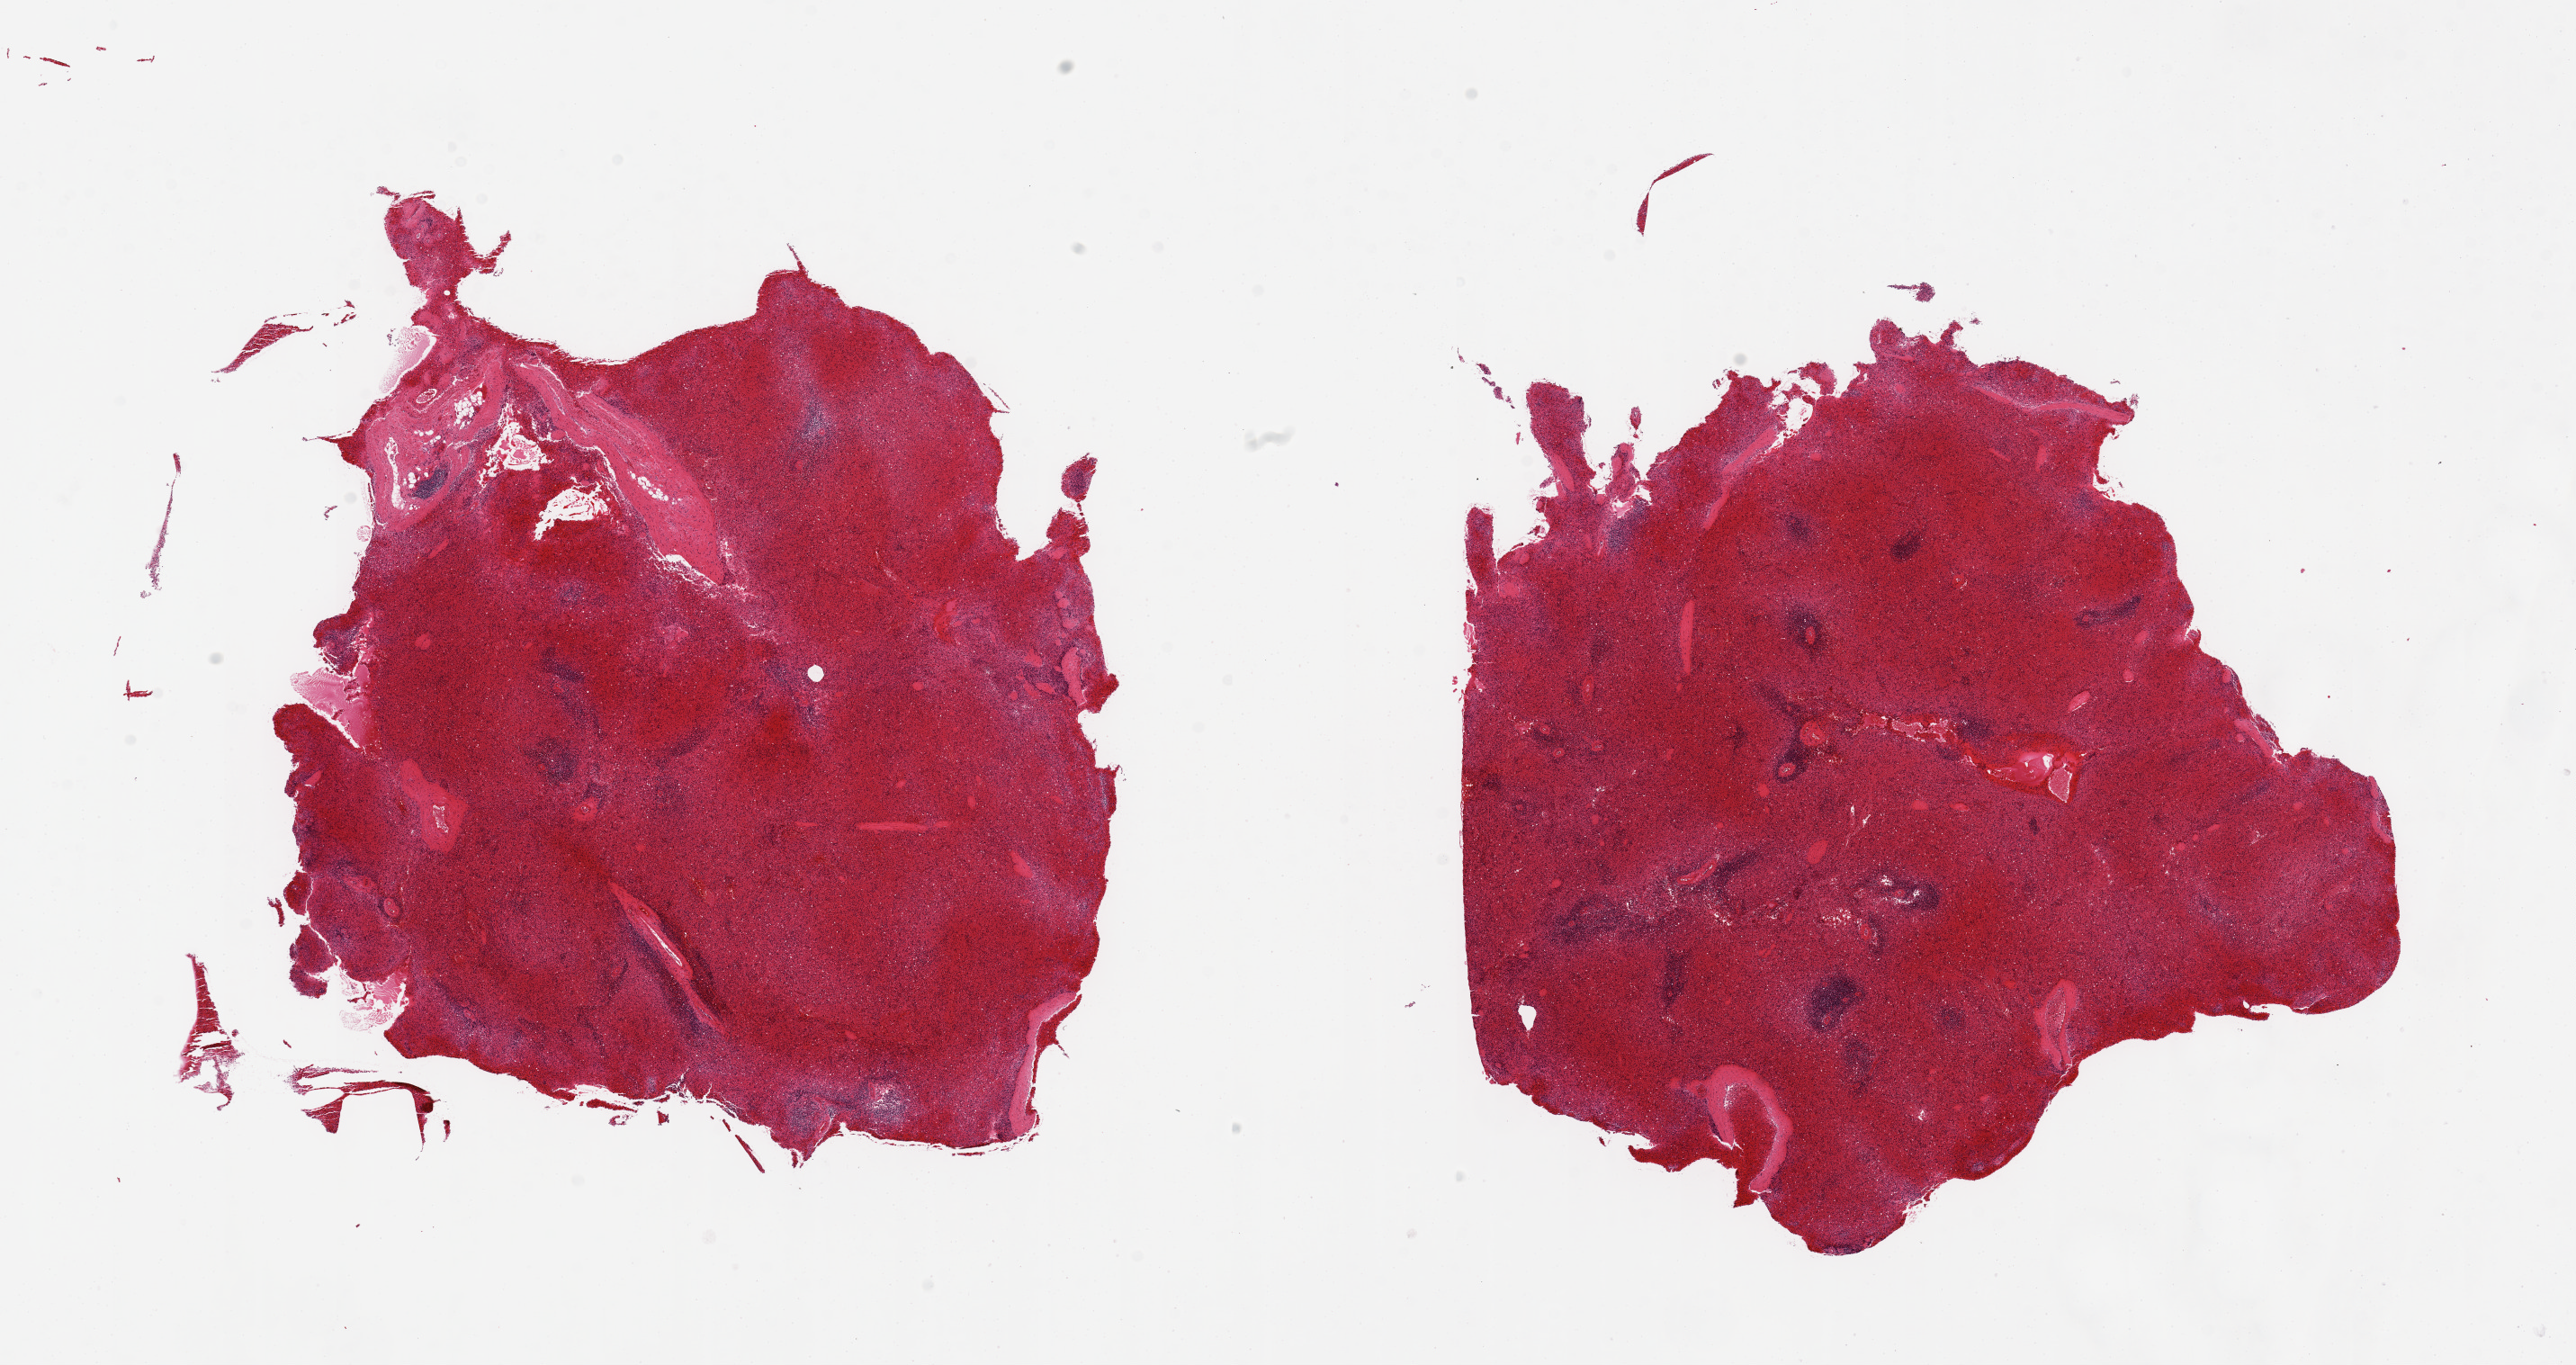
Digitized hematoxylin and eosin (H&E)-stained section — a low-resolution overview of the entire scanned area, about 22.6 x 12.0 mm; PAXgene-fixed paraffin-embedded (PFPE) section; sampled site (target tissue): spleen; tissue donor sample.
Review note (as recorded): 2 pieces, 9x8 & 10x8mm; badly autolyzed, congested.